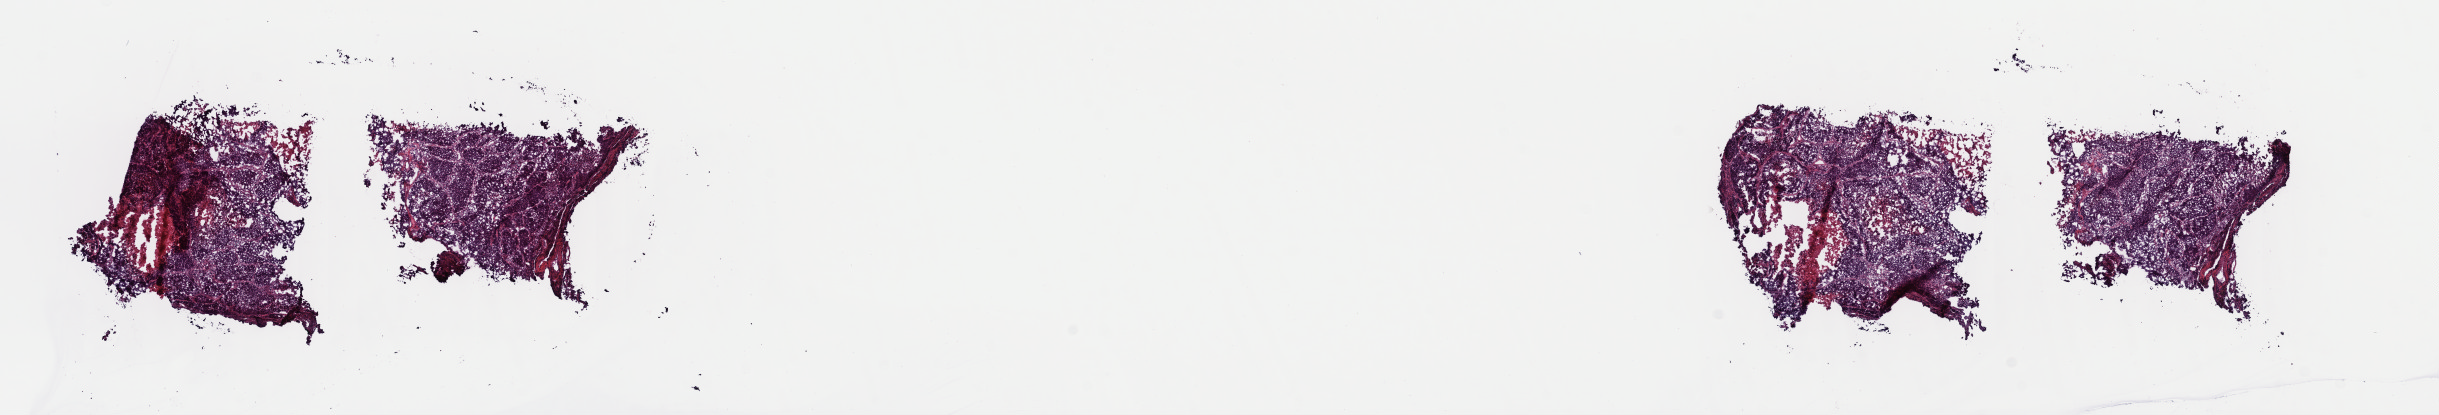
Whole-slide histology image, H&E, shown as a low-resolution overview of the whole scanned area (about 19.2 x 3.3 mm); frozen section from the top of the tissue portion; lung, primary tumour sample. Male patient; age at initial diagnosis 59 years. Slide review estimates, as recorded: tumour cells 80%, tumour nuclei 95%, normal cells 0%, stromal cells 10%, necrosis 10%. Inflammatory infiltration, as recorded: lymphocyte infiltration 2%, monocyte infiltration 4%, neutrophil infiltration 0%.
AJCC pathologic stage: IIB (6th edition). Diagnosis: Squamous cell carcinoma, NOS (middle lobe, lung).